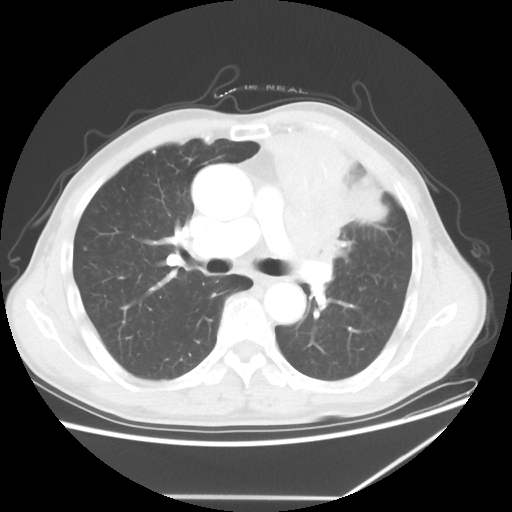
Chest CT, one axial slice. Slice 38 of 64 in the series (ordered by position). Reconstruction kernel STANDARD. Lung window (W 1500 / L -600 HU). 512 × 512 image matrix, field of view 383 × 383 mm. Patient: male, 64 years. From the clinical record (not read from this slice): clinical TNM (as recorded): T1c N1 M1; histopathological grade: G2.
Outlined on this slice (rectangle marked by the reading radiologist):
- lung tumour (recorded histology: squamous cell carcinoma): bounding box (x1, y1, x2, y2) in pixels: (252, 123, 395, 270)